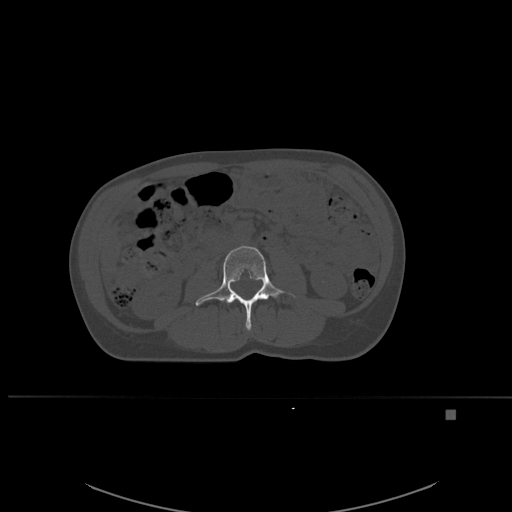
CT including the spine, one axial slice. Slice 215 of 537 in the series (ordered by position). Bone window (W 1800 / L 400 HU). 1.5 mm slice thickness. 512 × 512 image matrix, field of view 440 × 440 mm. Patient: female, 45 years. Case-level facts recorded for this patient, not image findings: primary cancer: lung.
Annotated regions visible in this slice (semi-automatic segmentation, software-assisted and operator-edited):
- L3 vertebra: bounding box (x1, y1, x2, y2) in pixels: (196, 245, 296, 330)